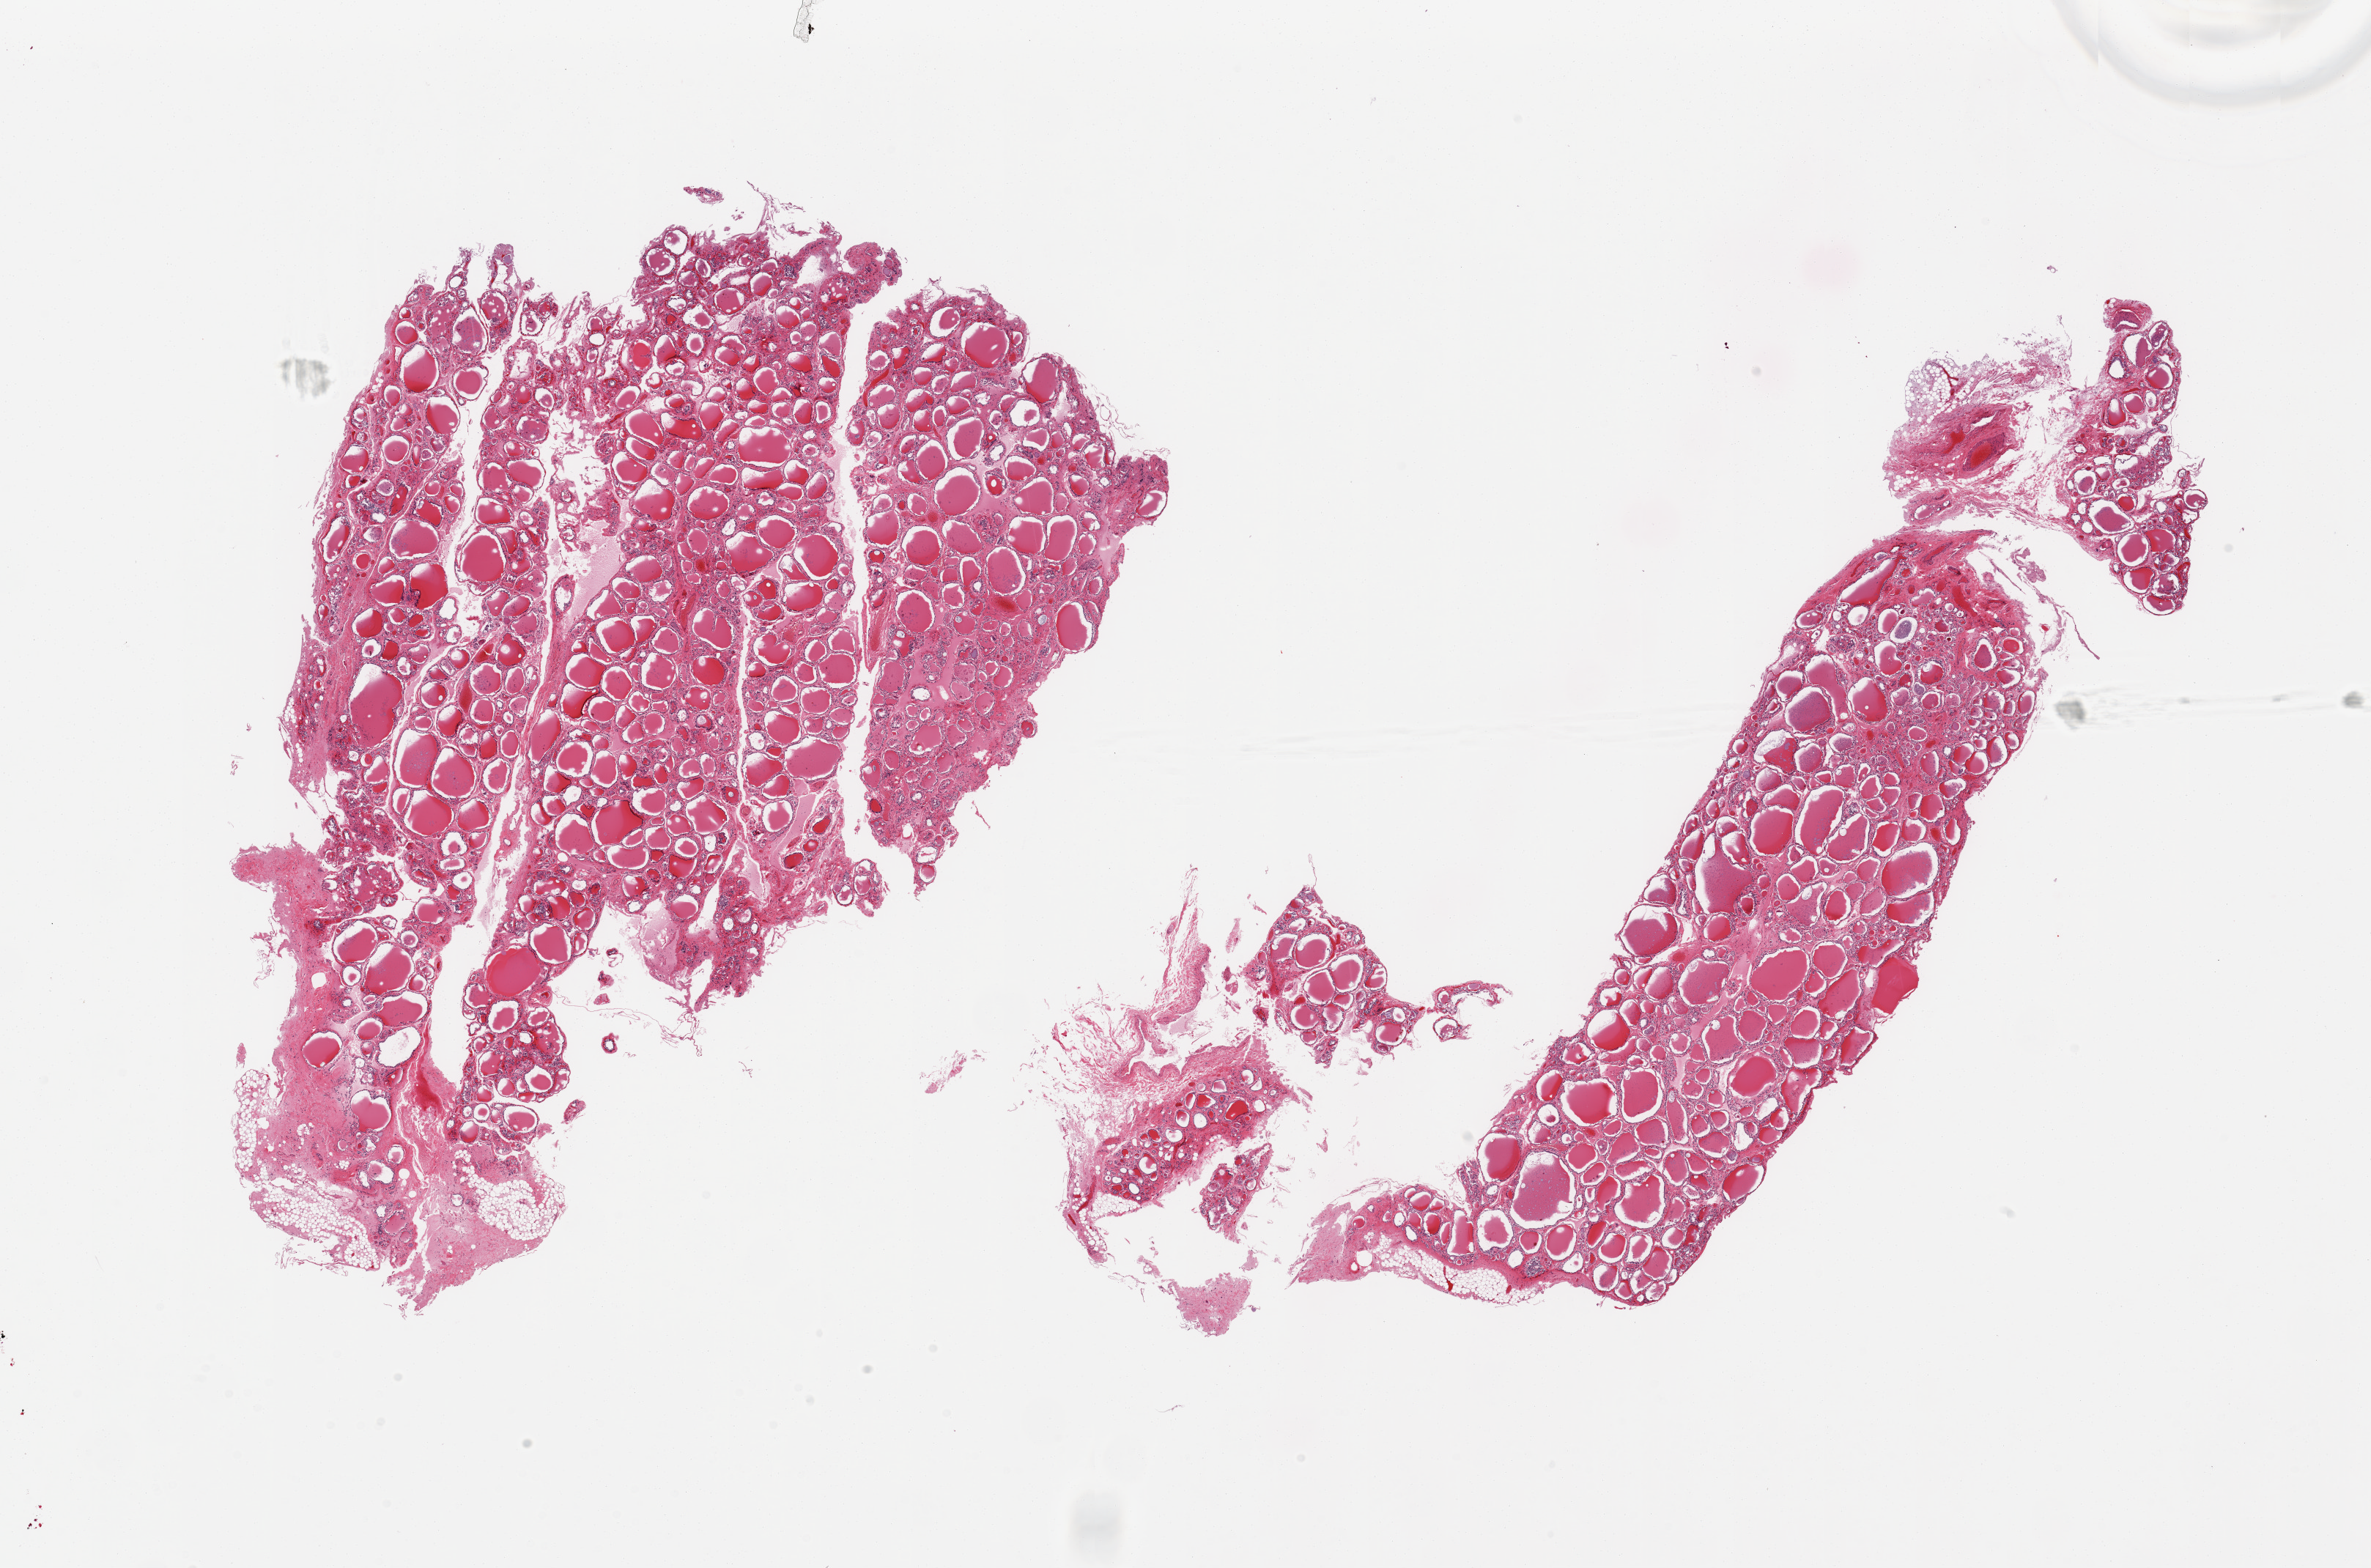
Haematoxylin and eosin whole-slide image — whole scanned area (about 25.6 x 16.9 mm, from a 20x scan) shown as a low-resolution overview; PAXgene-fixed, paraffin-embedded tissue; sampled site (target tissue): thyroid; donor tissue sample. Donor: male.
Reviewer comment on this tissue sample: 2 pieces, few fibrofatty nubbins up to 1.5mm.